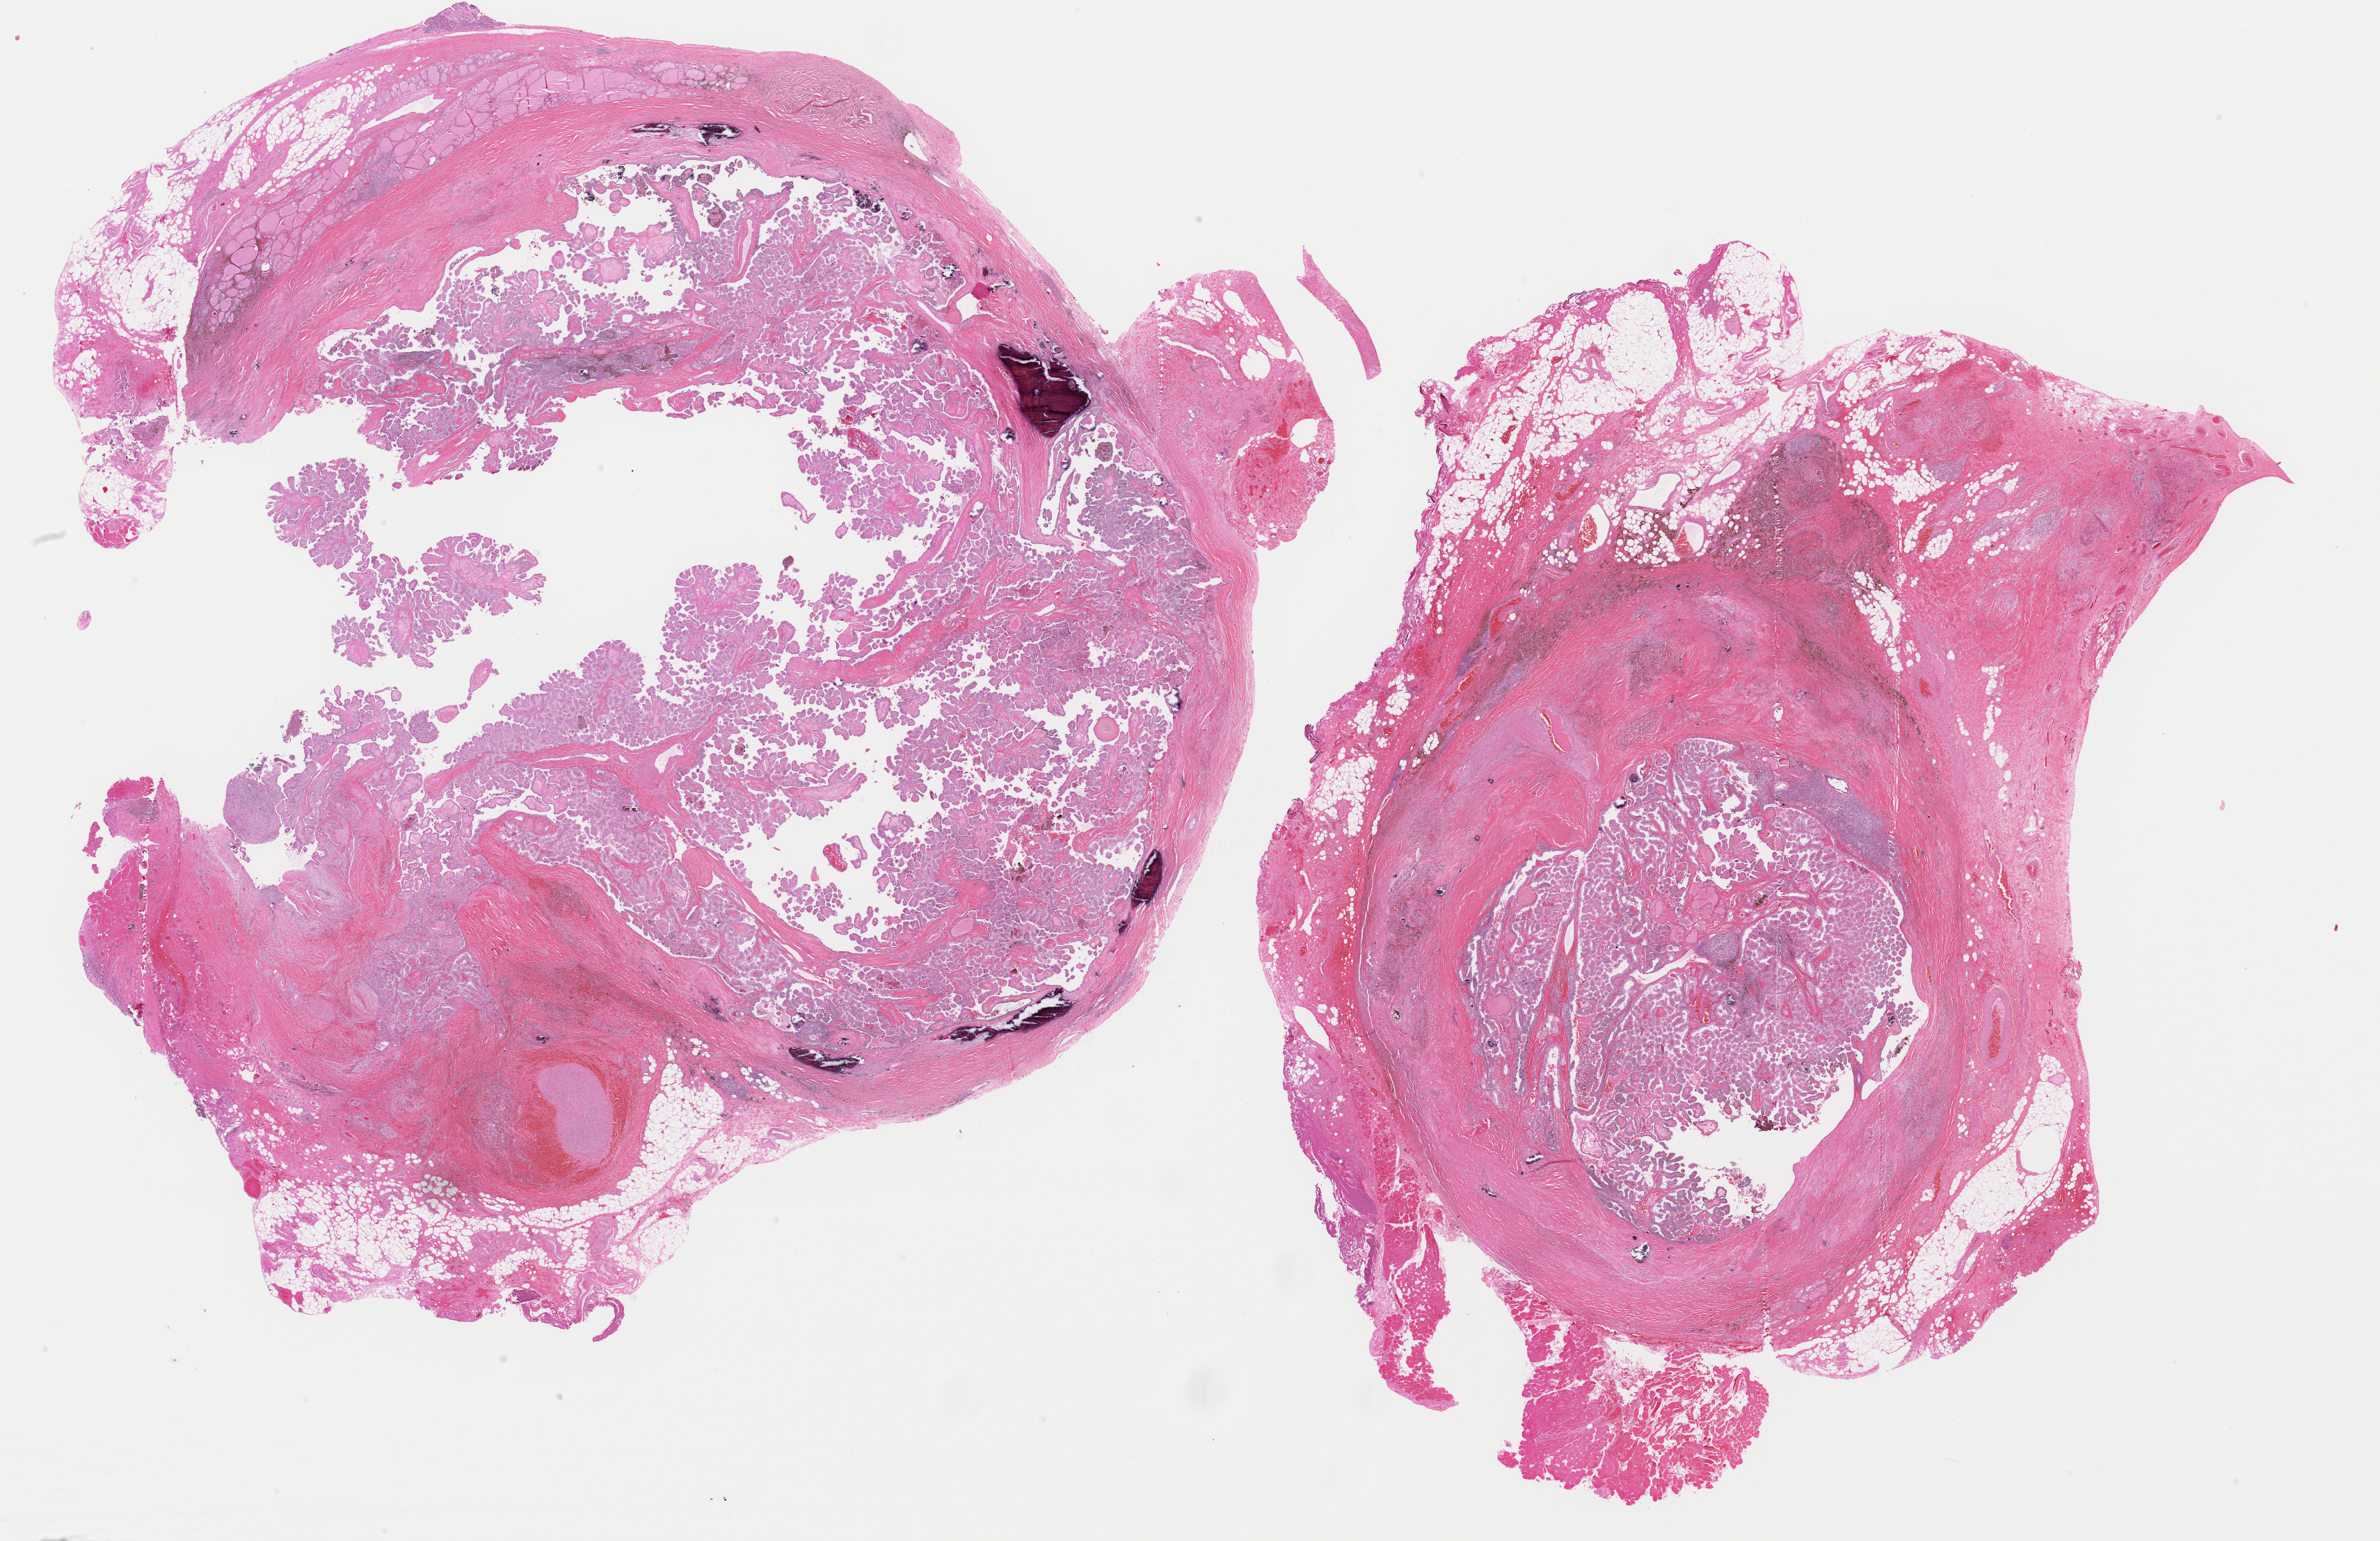
Digitized H&E tissue section (whole slide) — low-resolution overview of the scanned area, about 27.0 x 17.5 mm (acquisition: 40x scan), FFPE section, primary tumour sample from the thyroid. Patient: male, age at initial diagnosis 35 years.
TNM: T3 N0 M0. AJCC pathologic stage: I. Laterality: left. Diagnosis: Papillary adenocarcinoma, NOS (thyroid gland).